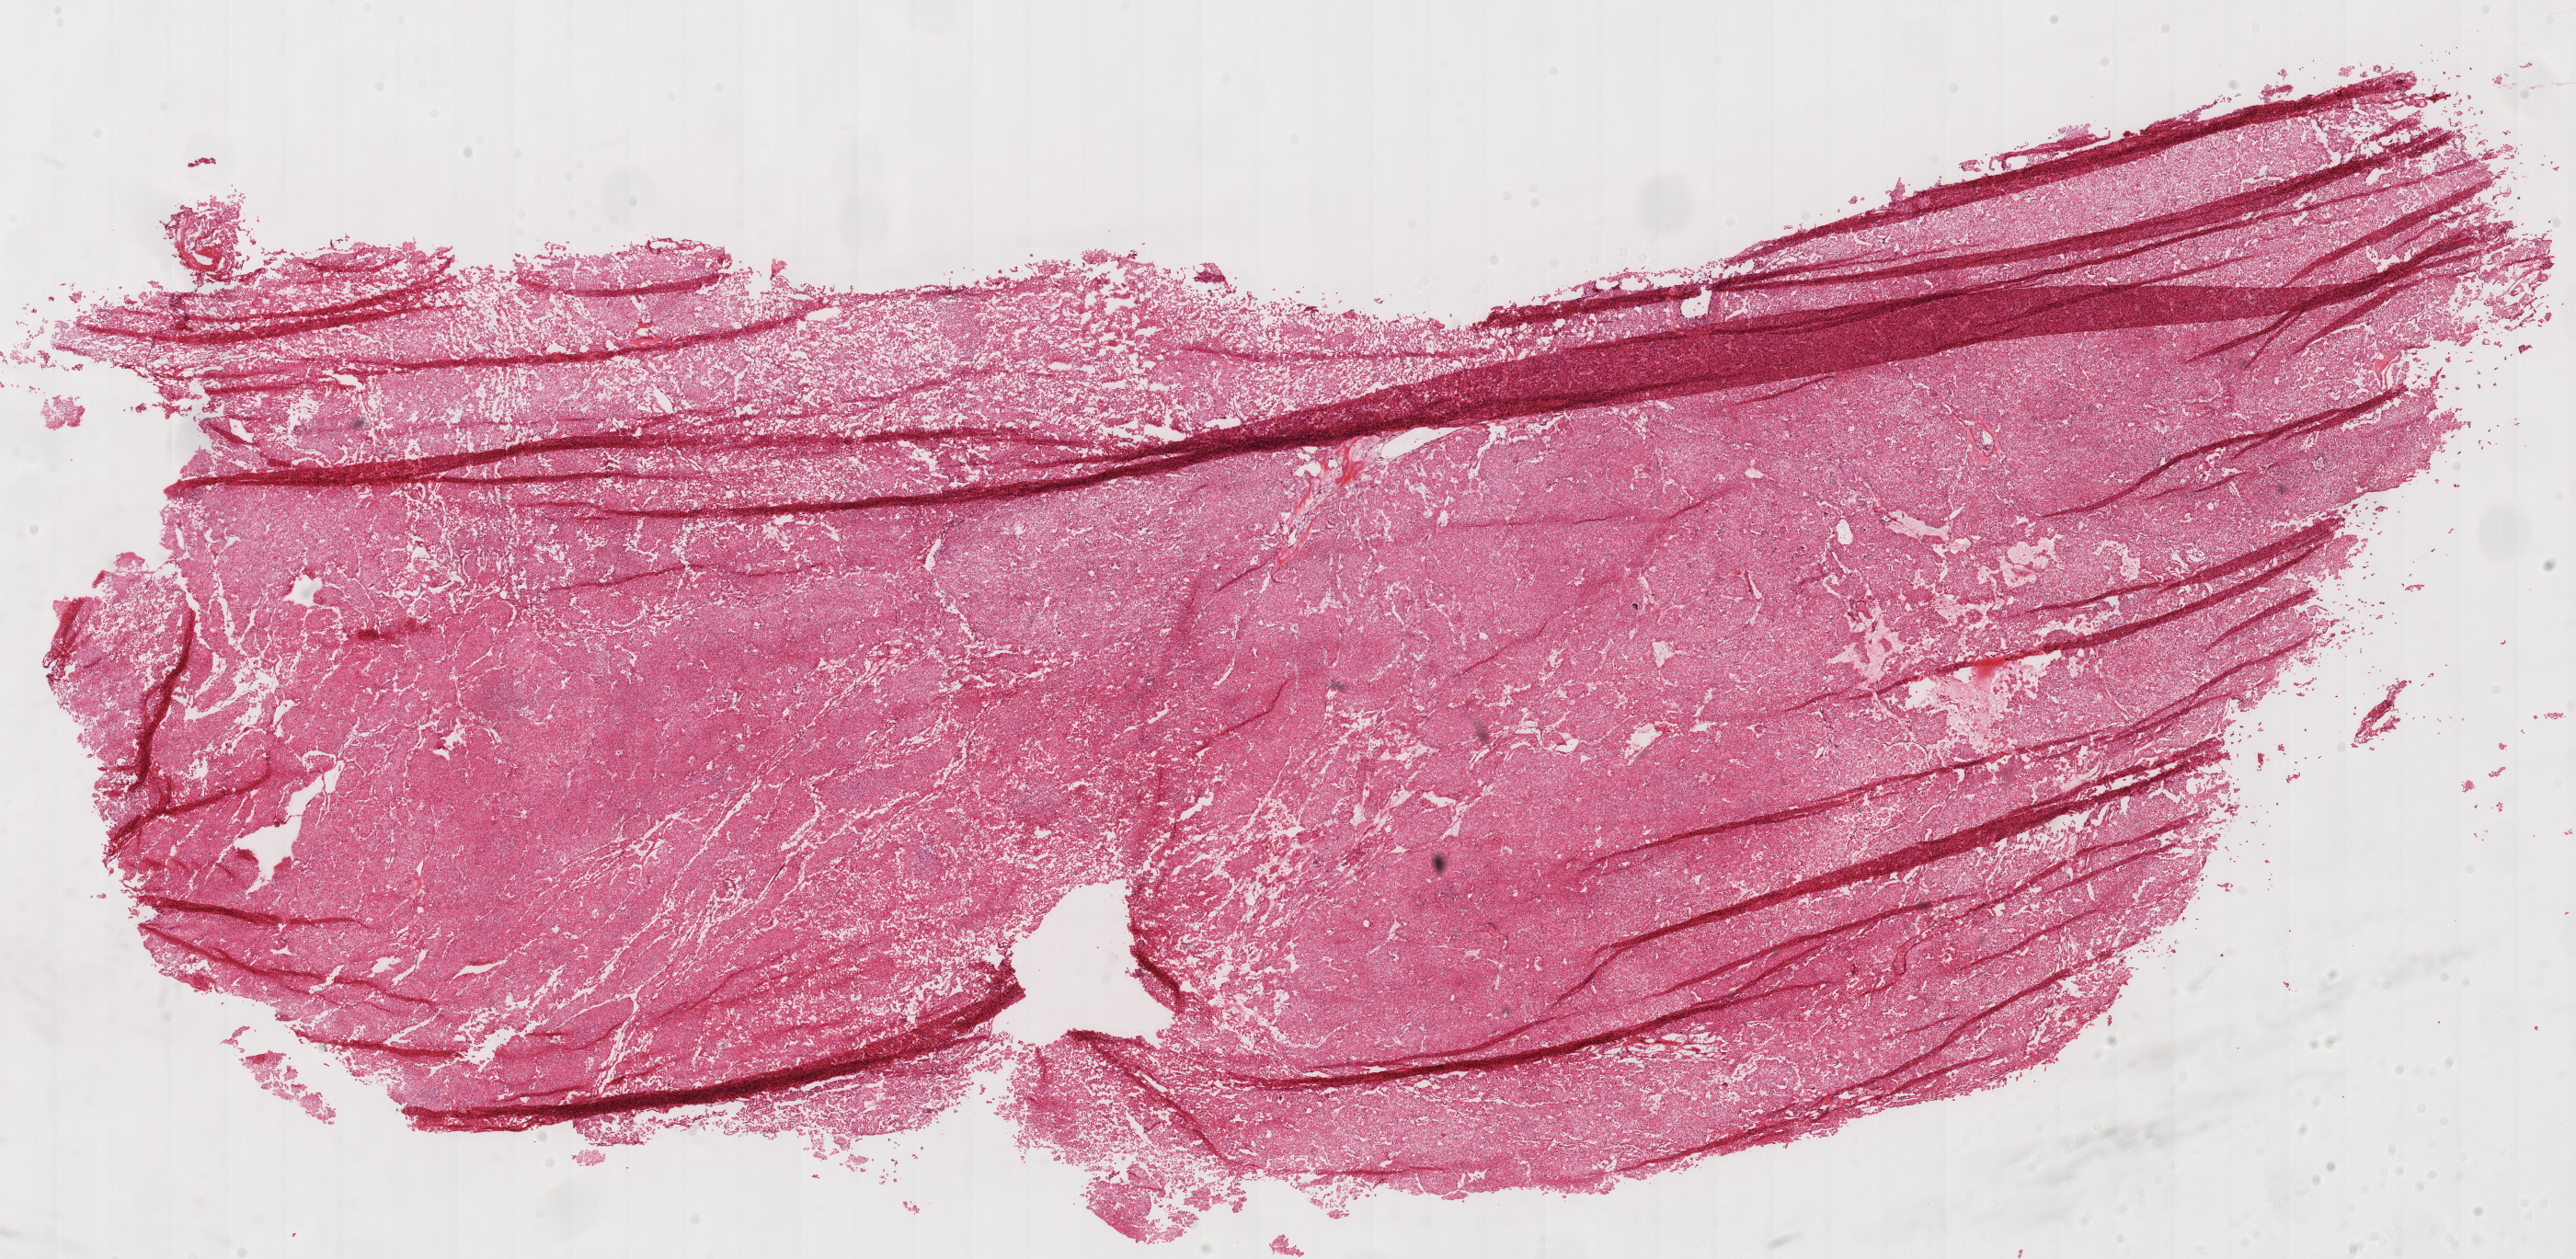
H&E whole-slide image — a low-resolution overview of the entire scanned area, about 22.0 x 10.8 mm (slide scanned at 40x), frozen section, kidney, primary tumour sample. Male, age 43 years at initial diagnosis. Composition of this section per pathologist review: tumour cells 100%, tumour nuclei 95%, normal cells 0%, stromal cells 0%, necrosis 0%. Inflammatory infiltration, as recorded: lymphocyte infiltration 0%, monocyte infiltration 0%, neutrophil infiltration 0%.
AJCC pathologic stage: II (6th edition). Histologic diagnosis: Renal cell carcinoma, chromophobe type.